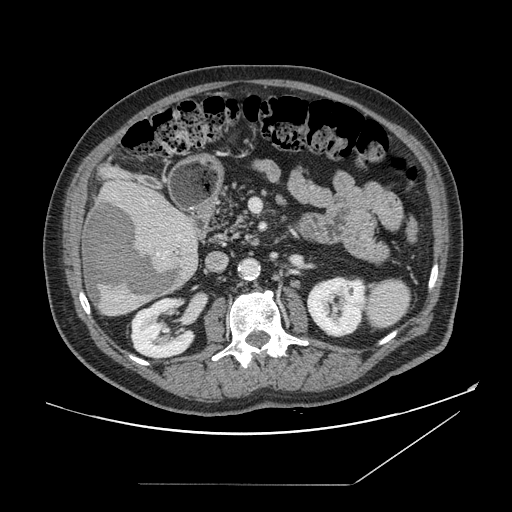
Contrast-enhanced abdominal CT, one axial slice. Position 68 of 166 along the scan axis. 120 kVp. Soft-tissue window (W 400 / L 40 HU). 2.5 mm slice thickness. 512 × 512 image matrix, field of view 416 × 416 mm. Male patient, age 80 years. From the clinical record (not read from this slice): diagnosis: colorectal cancer liver metastases, imaged before liver resection; multiple liver metastases: no; largest metastasis: 2.2 cm; chemotherapy before resection: no.
Structures marked on this image (manually delineated by an expert):
- liver: box from (x=82, y=179) to (x=199, y=317) px
- planned liver remnant (the part of the liver to remain after resection): (x=111, y=179)–(x=180, y=214)
- liver metastasis: (x=84, y=200)–(x=181, y=308)